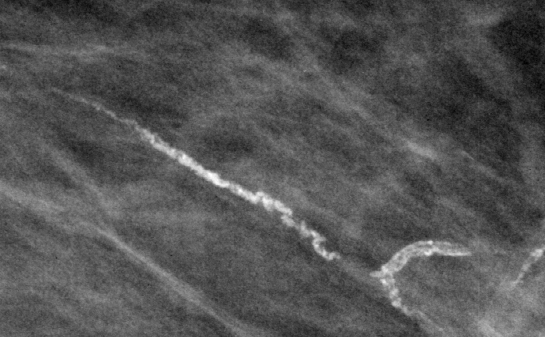
Region of interest cut from a scanned film mammogram (one marked finding), left breast, MLO view.
Marked abnormality: calcifications, morphology vascular; BI-RADS assessment category 2; benign without callback (not worked up further).